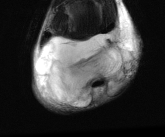
MRI of an extremity soft-tissue mass, one axial slice; position 16 of 81 along the scan axis; T2-weighted fat-saturated; MR volume resampled by the dataset authors to the PET/CT grid (not the native acquisition matrix); 165 × 137 image matrix, field of view 161 × 134 mm. Male patient. From the clinical record (not read from this slice): histological type: liposarcoma - round cell; grade: high; site of the primary tumour: right calf.
Outlined on this slice (expert contour drawn on MRI and transferred to this co-registered scan by the dataset authors):
- gross tumour volume (mass): bounding box <35,25,136,108> (left, top, right, bottom; pixels)